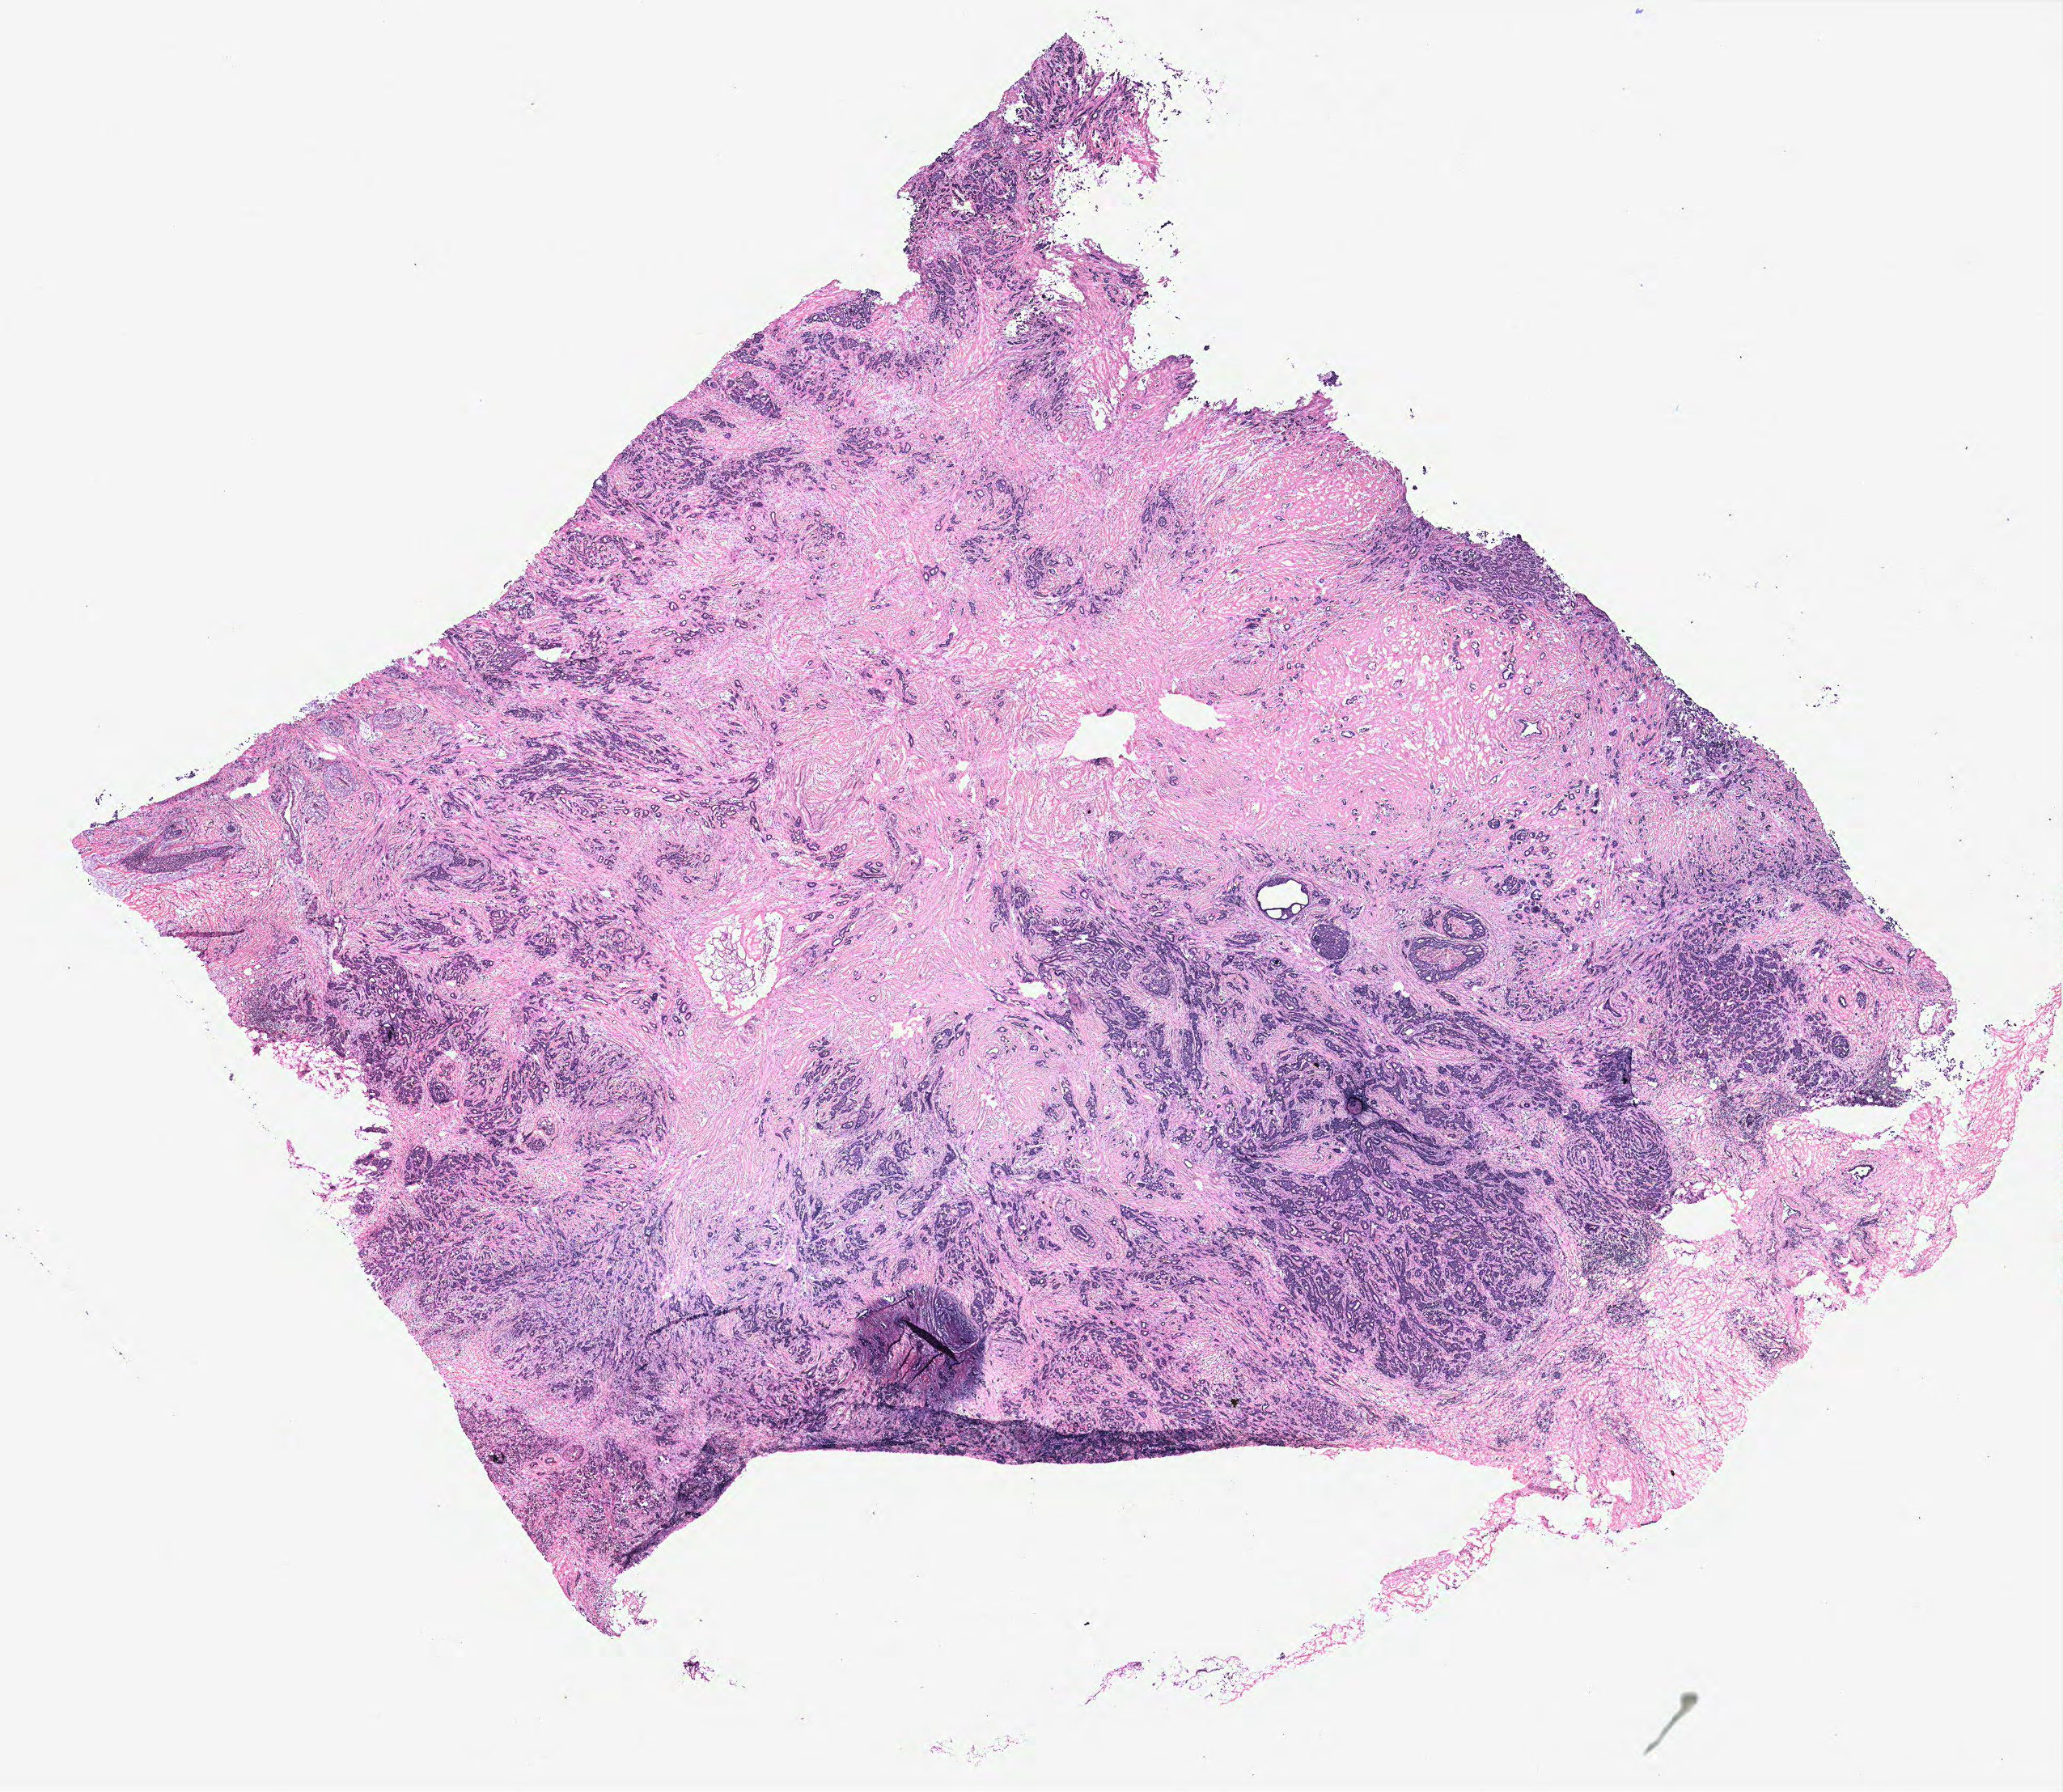
Whole-slide histology image, H&E, whole scanned area (about 20.4 x 17.7 mm) shown as a low-resolution overview, tumour tissue sample, breast. 66-year-old female patient.
AJCC pathologic stage: IIIA. Diagnosis: Infiltrating duct carcinoma, NOS.